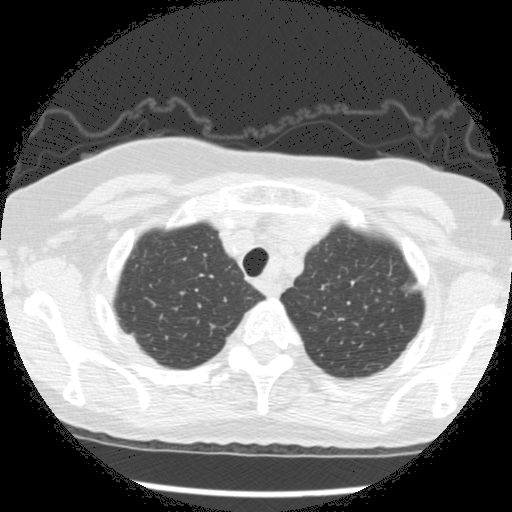
Chest CT (low-dose screening protocol), one axial image. Second screening round (one year after baseline). Lung window (W 1500 / L -600 HU). 2.5 mm slice thickness. Standard (soft-tissue) reconstruction kernel (STANDARD). 512 × 512 image matrix, field of view 320 × 320 mm. Female, age 73 years at enrolment.
Expert reader's lesion annotation, bounding box [x1, y1, x2, y2] px = [383, 254, 430, 302]. The screening reader recorded 3 non-calcified nodules or masses ≥4 mm on this exam (left upper lobe, left upper lobe, left upper lobe); which of them this box marks is not recorded. Official screen result: positive, change unspecified: nodule(s) >= 4 mm or enlarging nodule(s), mass(es), or other non-specific abnormalities suspicious for lung cancer. Later outcome: lung cancer diagnosed 49 days after this screen — bronchiolo-alveolar adenocarcinoma, NOS, left upper lobe, well differentiated (G1), stage IA (AJCC 6th edition), 10 mm at pathology.